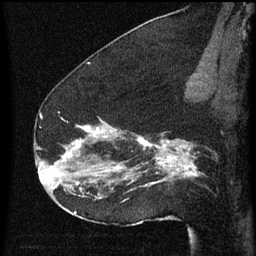
Breast MRI (dynamic contrast-enhanced), one sagittal slice. Position 38 of 60 along the scan axis. Dynamic contrast-enhanced series, image 2 of 3 at this slice position (ordered by acquisition). 1.5 T. TE 4.2 ms, TR 8 ms. 2 mm slice thickness. 256 × 256 image matrix. Female patient, age 52 years.
Annotated regions visible in this slice (semi-automatically segmented with operator editing):
- analysis volume of interest (the breast-tissue region the enhancement analysis was run in; not a lesion): box from (x=54, y=112) to (x=178, y=207) px
- tumour enhancement mask (voxels above the 70 % enhancement threshold inside the analysis volume of interest): (x=65, y=128)–(x=178, y=187)